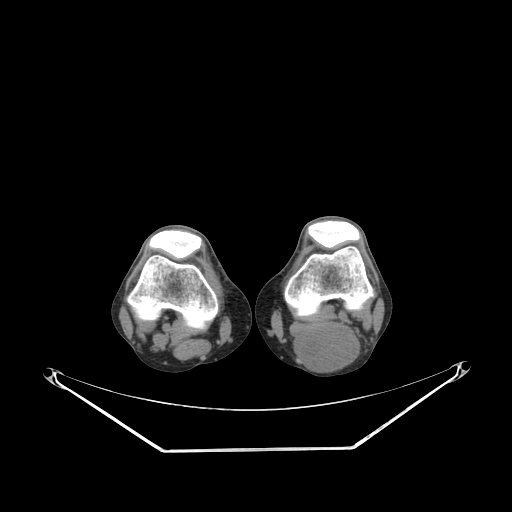
CT of an extremity soft-tissue mass (from a PET/CT study), one axial slice; reconstruction kernel SOFT; 140 kVp; soft-tissue window (W 400 / L 40 HU); 3.75 mm slice thickness; 512 × 512 image matrix, field of view 500 × 500 mm. Male patient. From the clinical record (not read from this slice): histological type: synovial sarcoma; site of the primary tumour: left poplietal fossa.
Structures marked on this image (expert contour drawn on MRI and transferred to this co-registered scan by the dataset authors):
- gross tumour volume (mass): bounding box <292,326,362,371> (left, top, right, bottom; pixels)